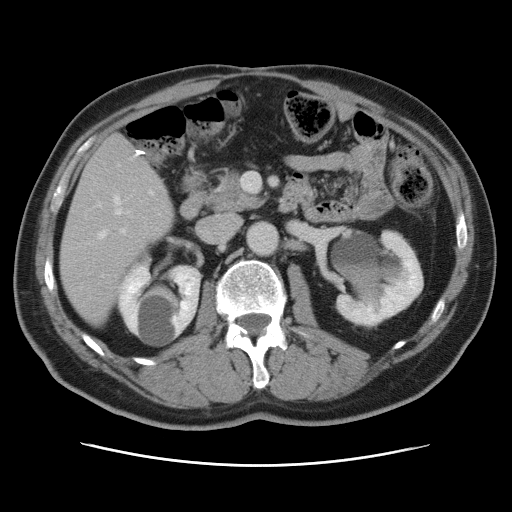
Contrast-enhanced abdominal CT, one axial slice; position 33 of 80 along the scan axis; soft-tissue window (W 400 / L 40 HU); 5 mm slice thickness; 512 × 512 image matrix. Male patient, age 69 years. From the clinical record (not read from this slice): diagnosis: colorectal cancer liver metastases, imaged before liver resection; multiple liver metastases: no; largest metastasis: 5 cm; disease in both lobes: yes.
Outlined on this slice (manually delineated by an expert):
- hepatic veins: bounding box [x1, y1, x2, y2] px = [98, 196, 121, 239]
- liver: [61, 135, 173, 322]
- planned liver remnant (the part of the liver to remain after resection): [61, 210, 172, 322]
- portal vein (with intrahepatic branches): [101, 192, 152, 277]